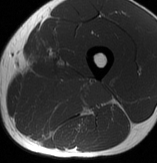
MRI of an extremity soft-tissue mass, one axial slice; slice 32 of 70 in the series (ordered by position); MR volume resampled by the dataset authors to the PET/CT grid (not the native acquisition matrix); 157 × 163 image matrix. Male patient. From the clinical record (not read from this slice): histological type: extraskeletal osteosarcoma; grade: high; site of the primary tumour: left adductur.
Outlined on this slice (expert contour drawn on MRI and transferred to this co-registered scan by the dataset authors):
- gross tumour volume (mass): bounding box <13,71,112,137> (left, top, right, bottom; pixels)